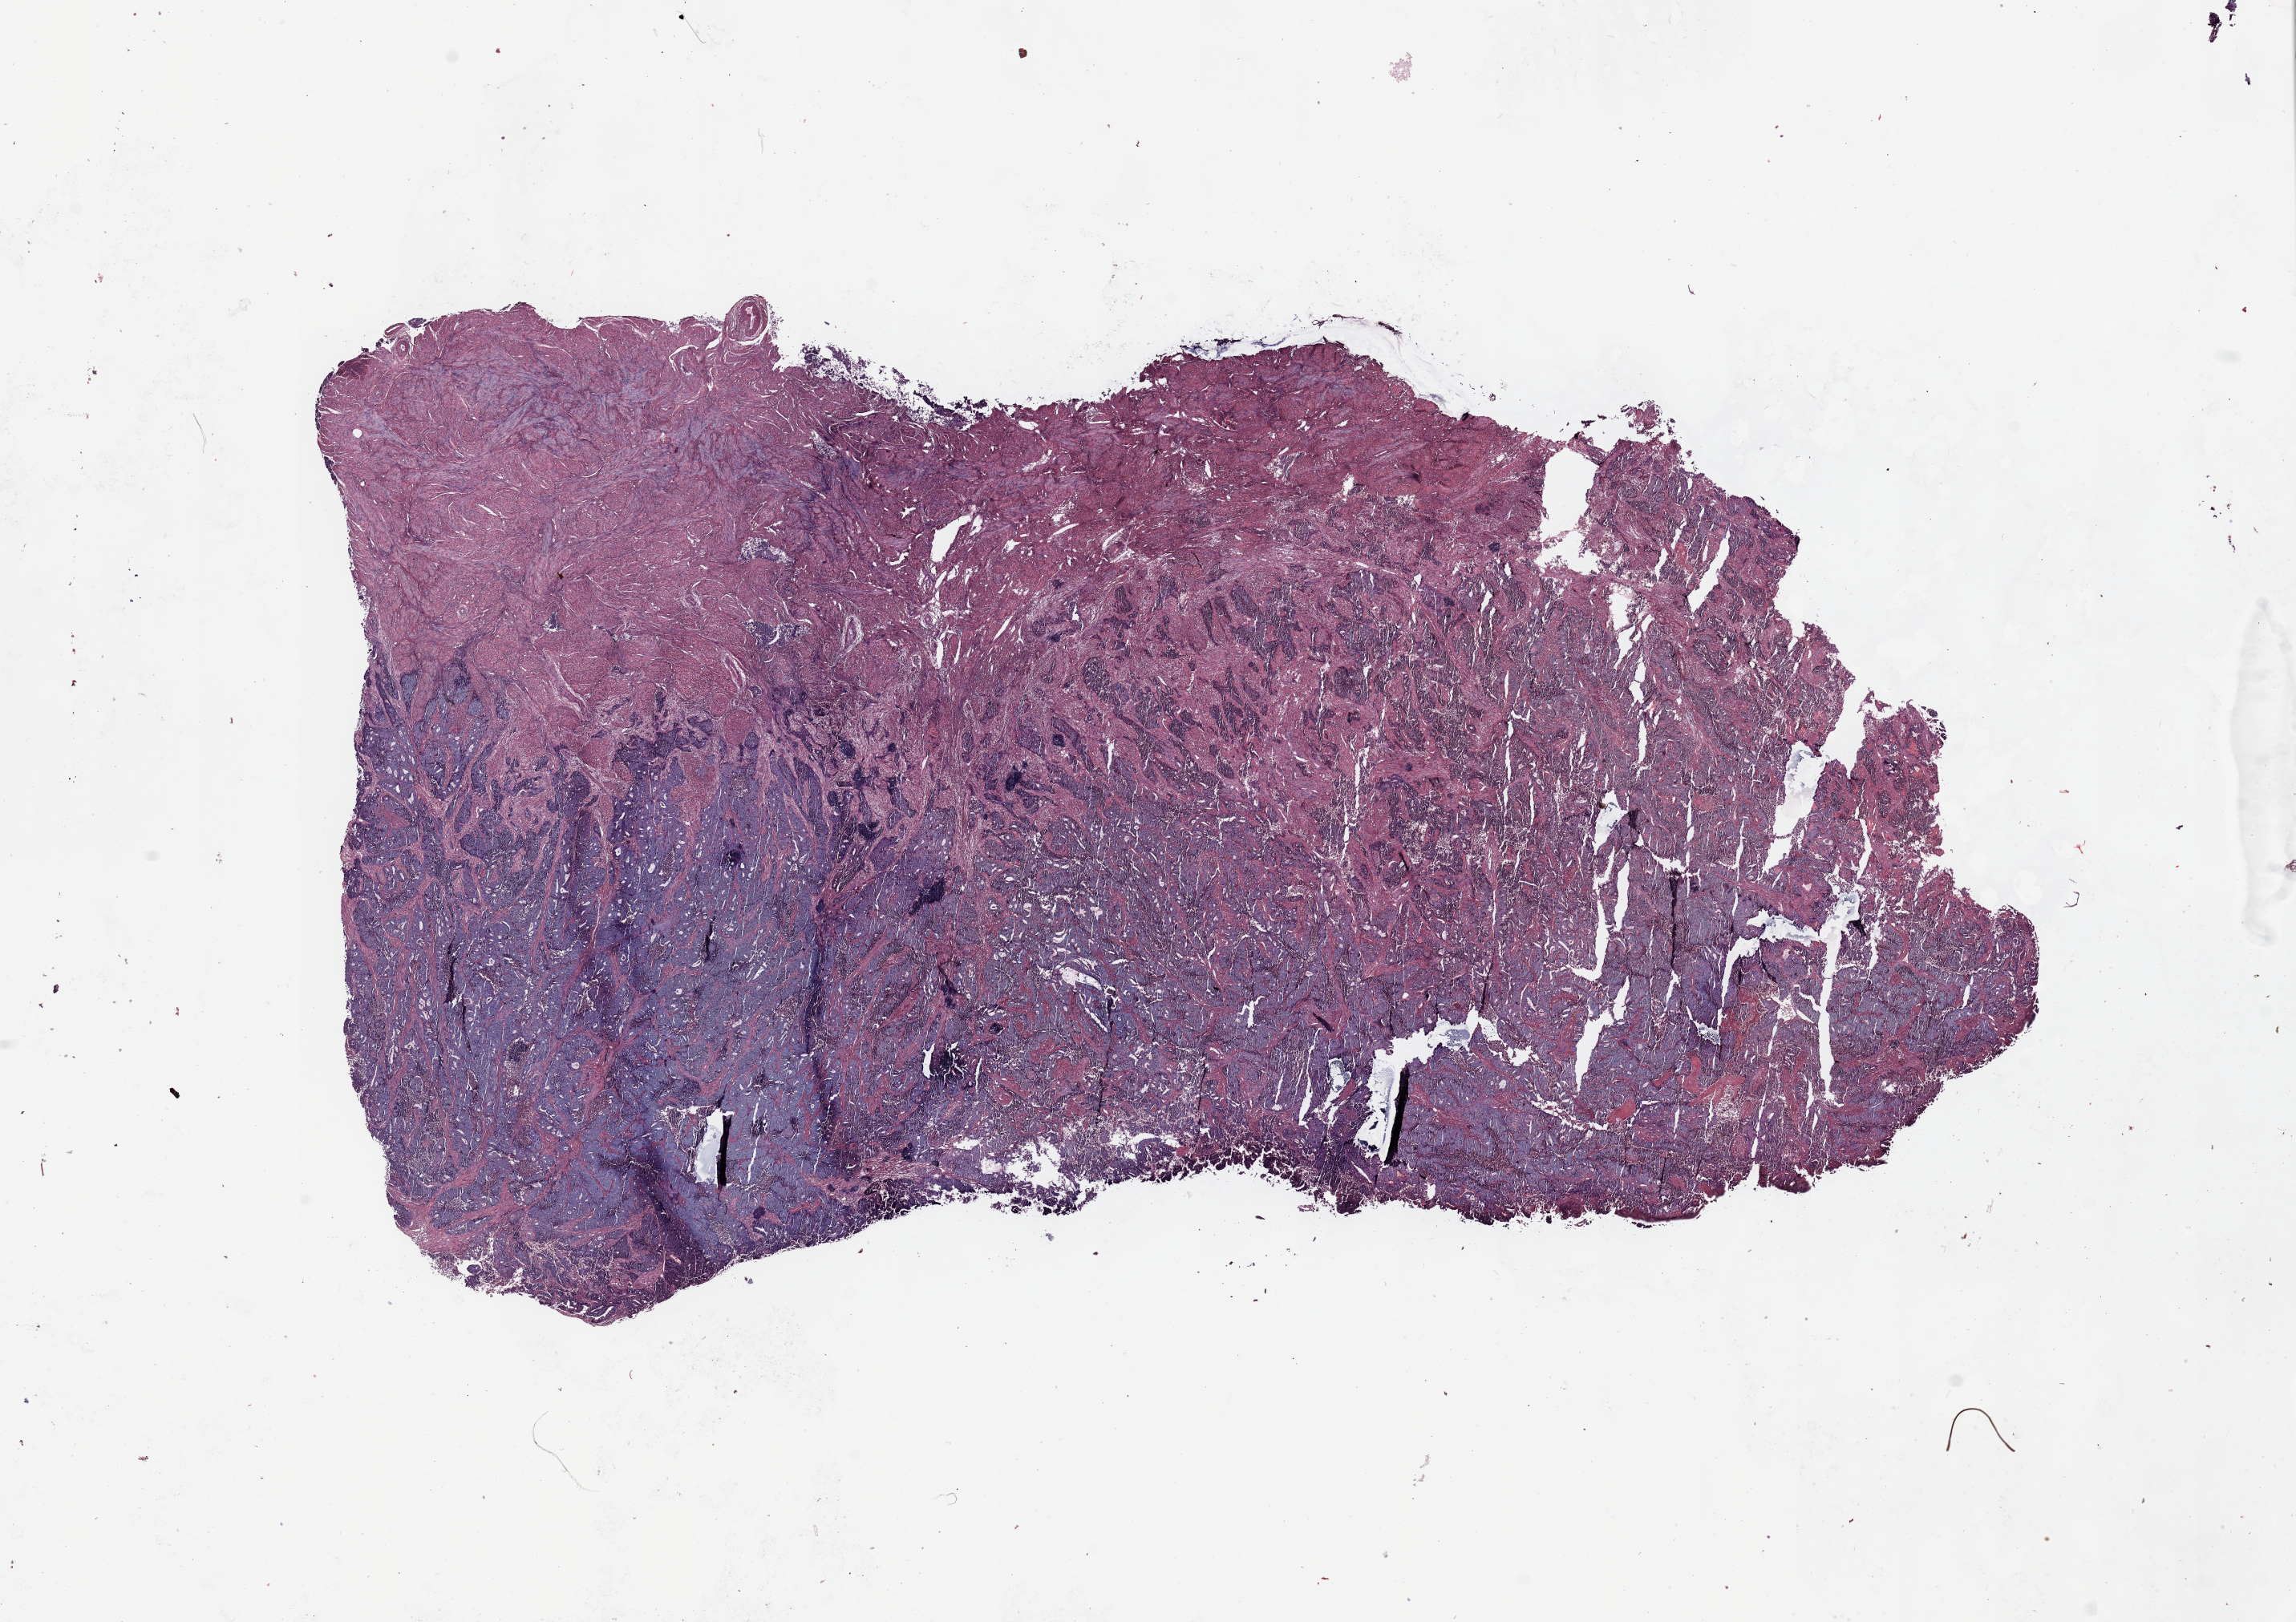
Whole-slide histology image, Hematoxylin and eosin (H&E) stained — a low-resolution overview of the entire scanned area, about 22.6 x 16.0 mm; tumour tissue sample, sampled site: uterus. Patient: female, age 59 years. Histologic grade: G2 (moderately differentiated). Composition of this section per pathologist review: tumour nuclei 80%, necrosis 2%.
Diagnosis: Endometrioid adenocarcinoma, NOS. AJCC pathologic stage: II.